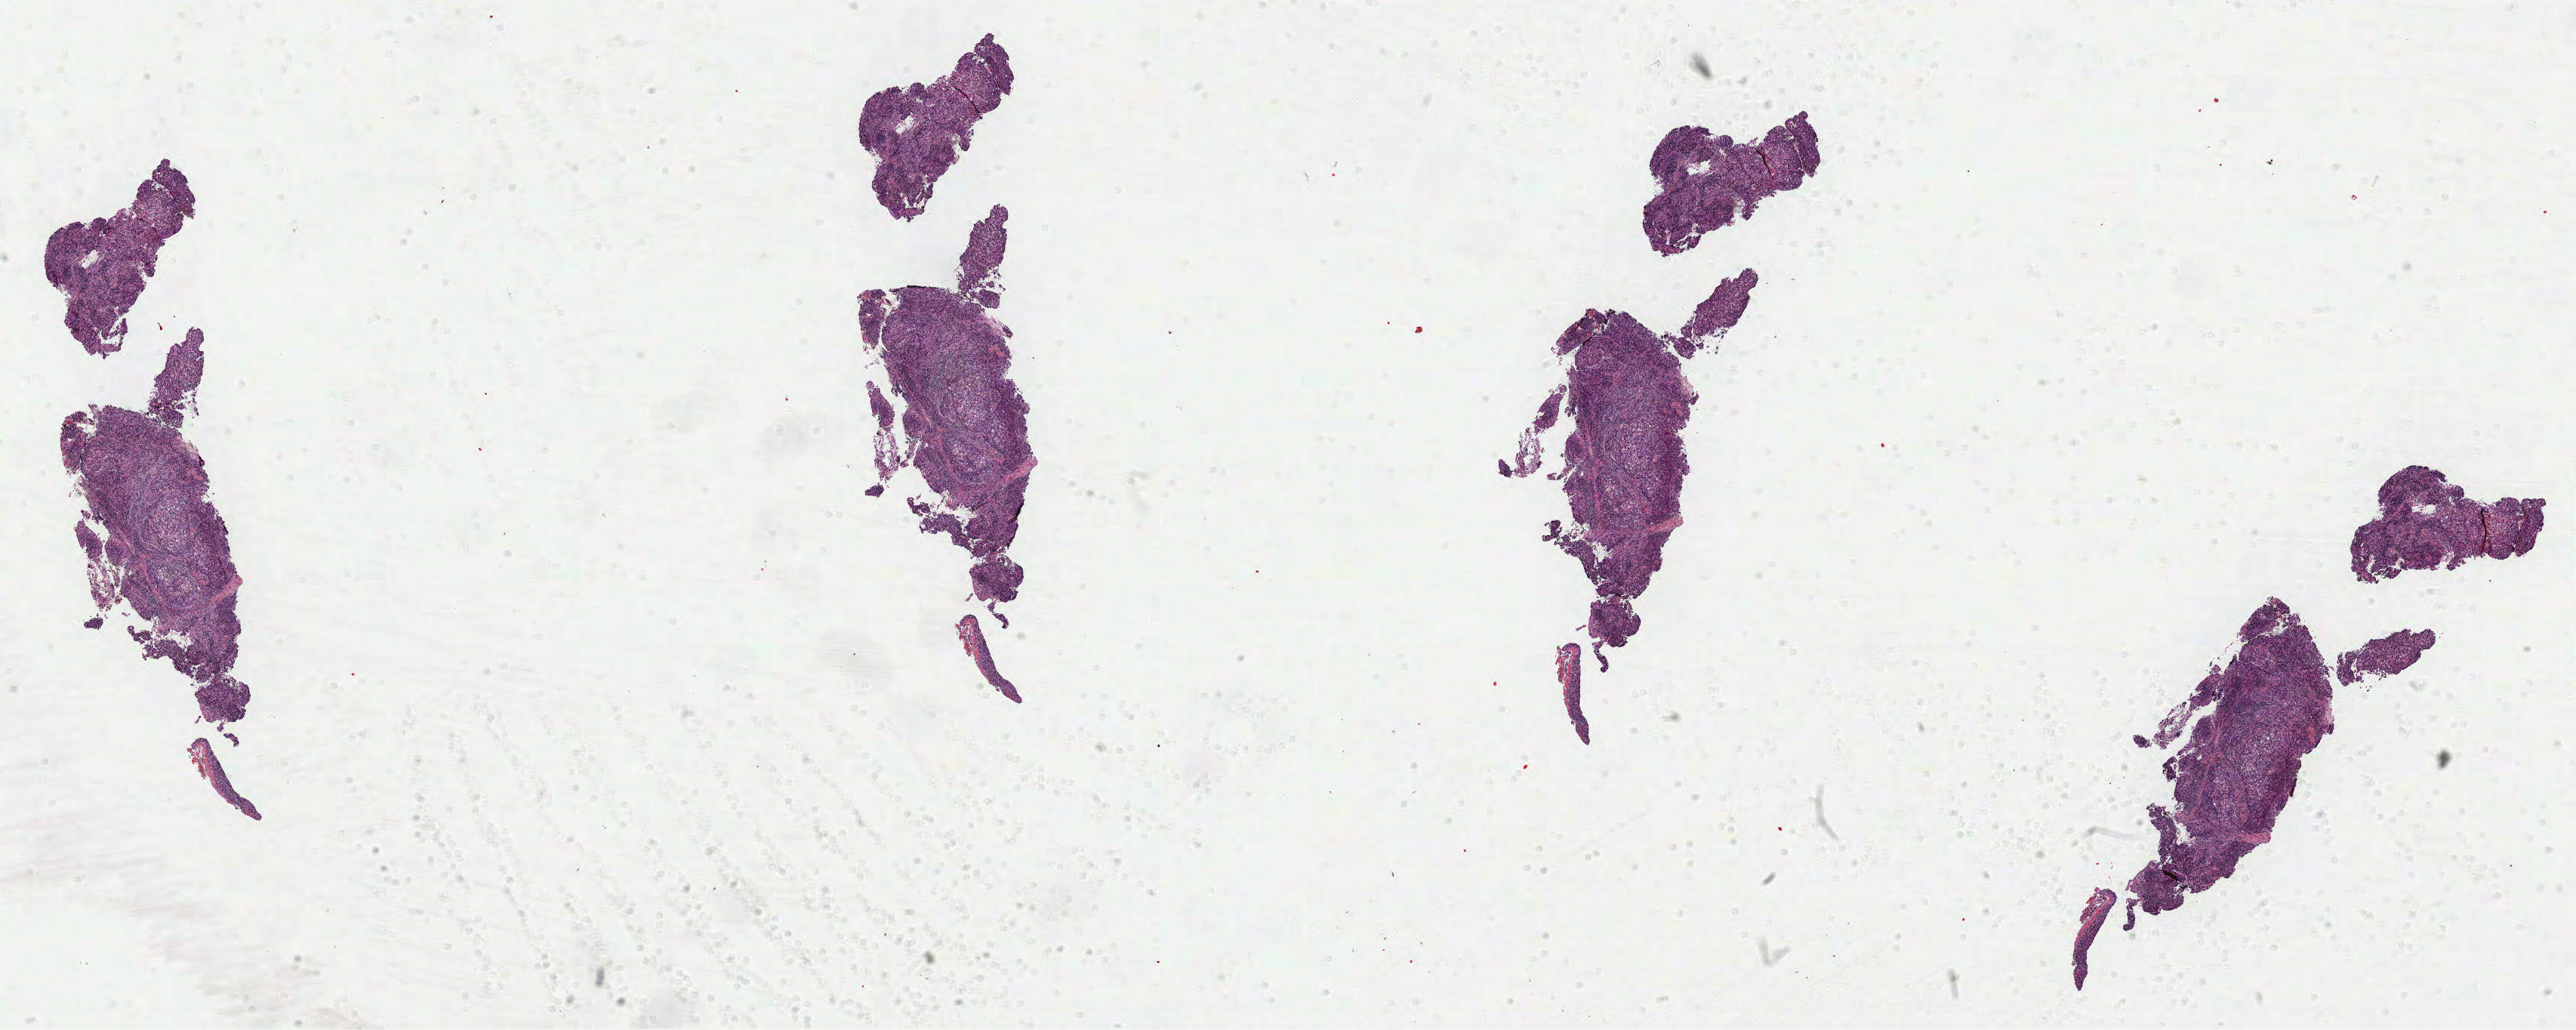
H&E whole-slide image — a low-resolution overview of the entire scanned area, about 27.5 x 11.0 mm (from a 40x scan). FFPE section. Primary tumour sample from the cervix. Female, age 85 years at initial diagnosis.
Histologic diagnosis: Squamous cell carcinoma, large cell, nonkeratinizing, NOS (cervix uteri).